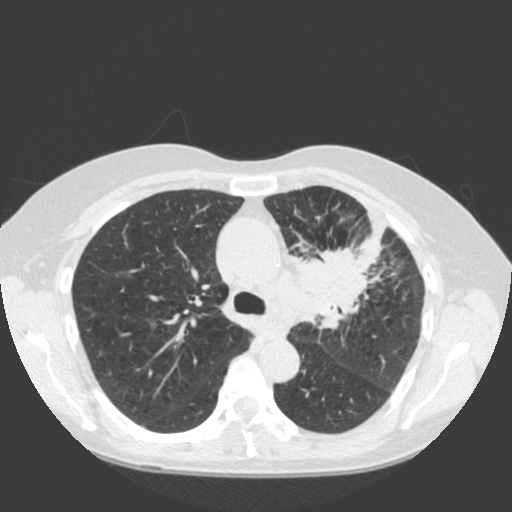
Chest CT (low-dose screening protocol), one axial image; baseline annual screen; lung window (W 1500 / L -600 HU); 120 kVp; slice 55 of 184 in the series. Female participant, aged 66 years at enrolment.
Expert-annotated lung lesion, bounding box [x1, y1, x2, y2] px = [283, 230, 399, 333]. Reader record for this screening exam (exam-level; its link to the box is not recorded): non-calcified nodule or mass ≥4 mm, left upper lobe, 61 × 45 mm, spiculated (stellate) margins, soft tissue attenuation. Official screen result: positive, change unspecified: nodule(s) >= 4 mm or enlarging nodule(s), mass(es), or other non-specific abnormalities suspicious for lung cancer. Lung cancer was diagnosed 19 days after this screen: squamous cell carcinoma, keratinizing, NOS, left upper lobe, left hilum, mediastinum, left main stem bronchus, other location, poorly differentiated (G3), stage IIIB (AJCC 6th edition), 60 mm at pathology.